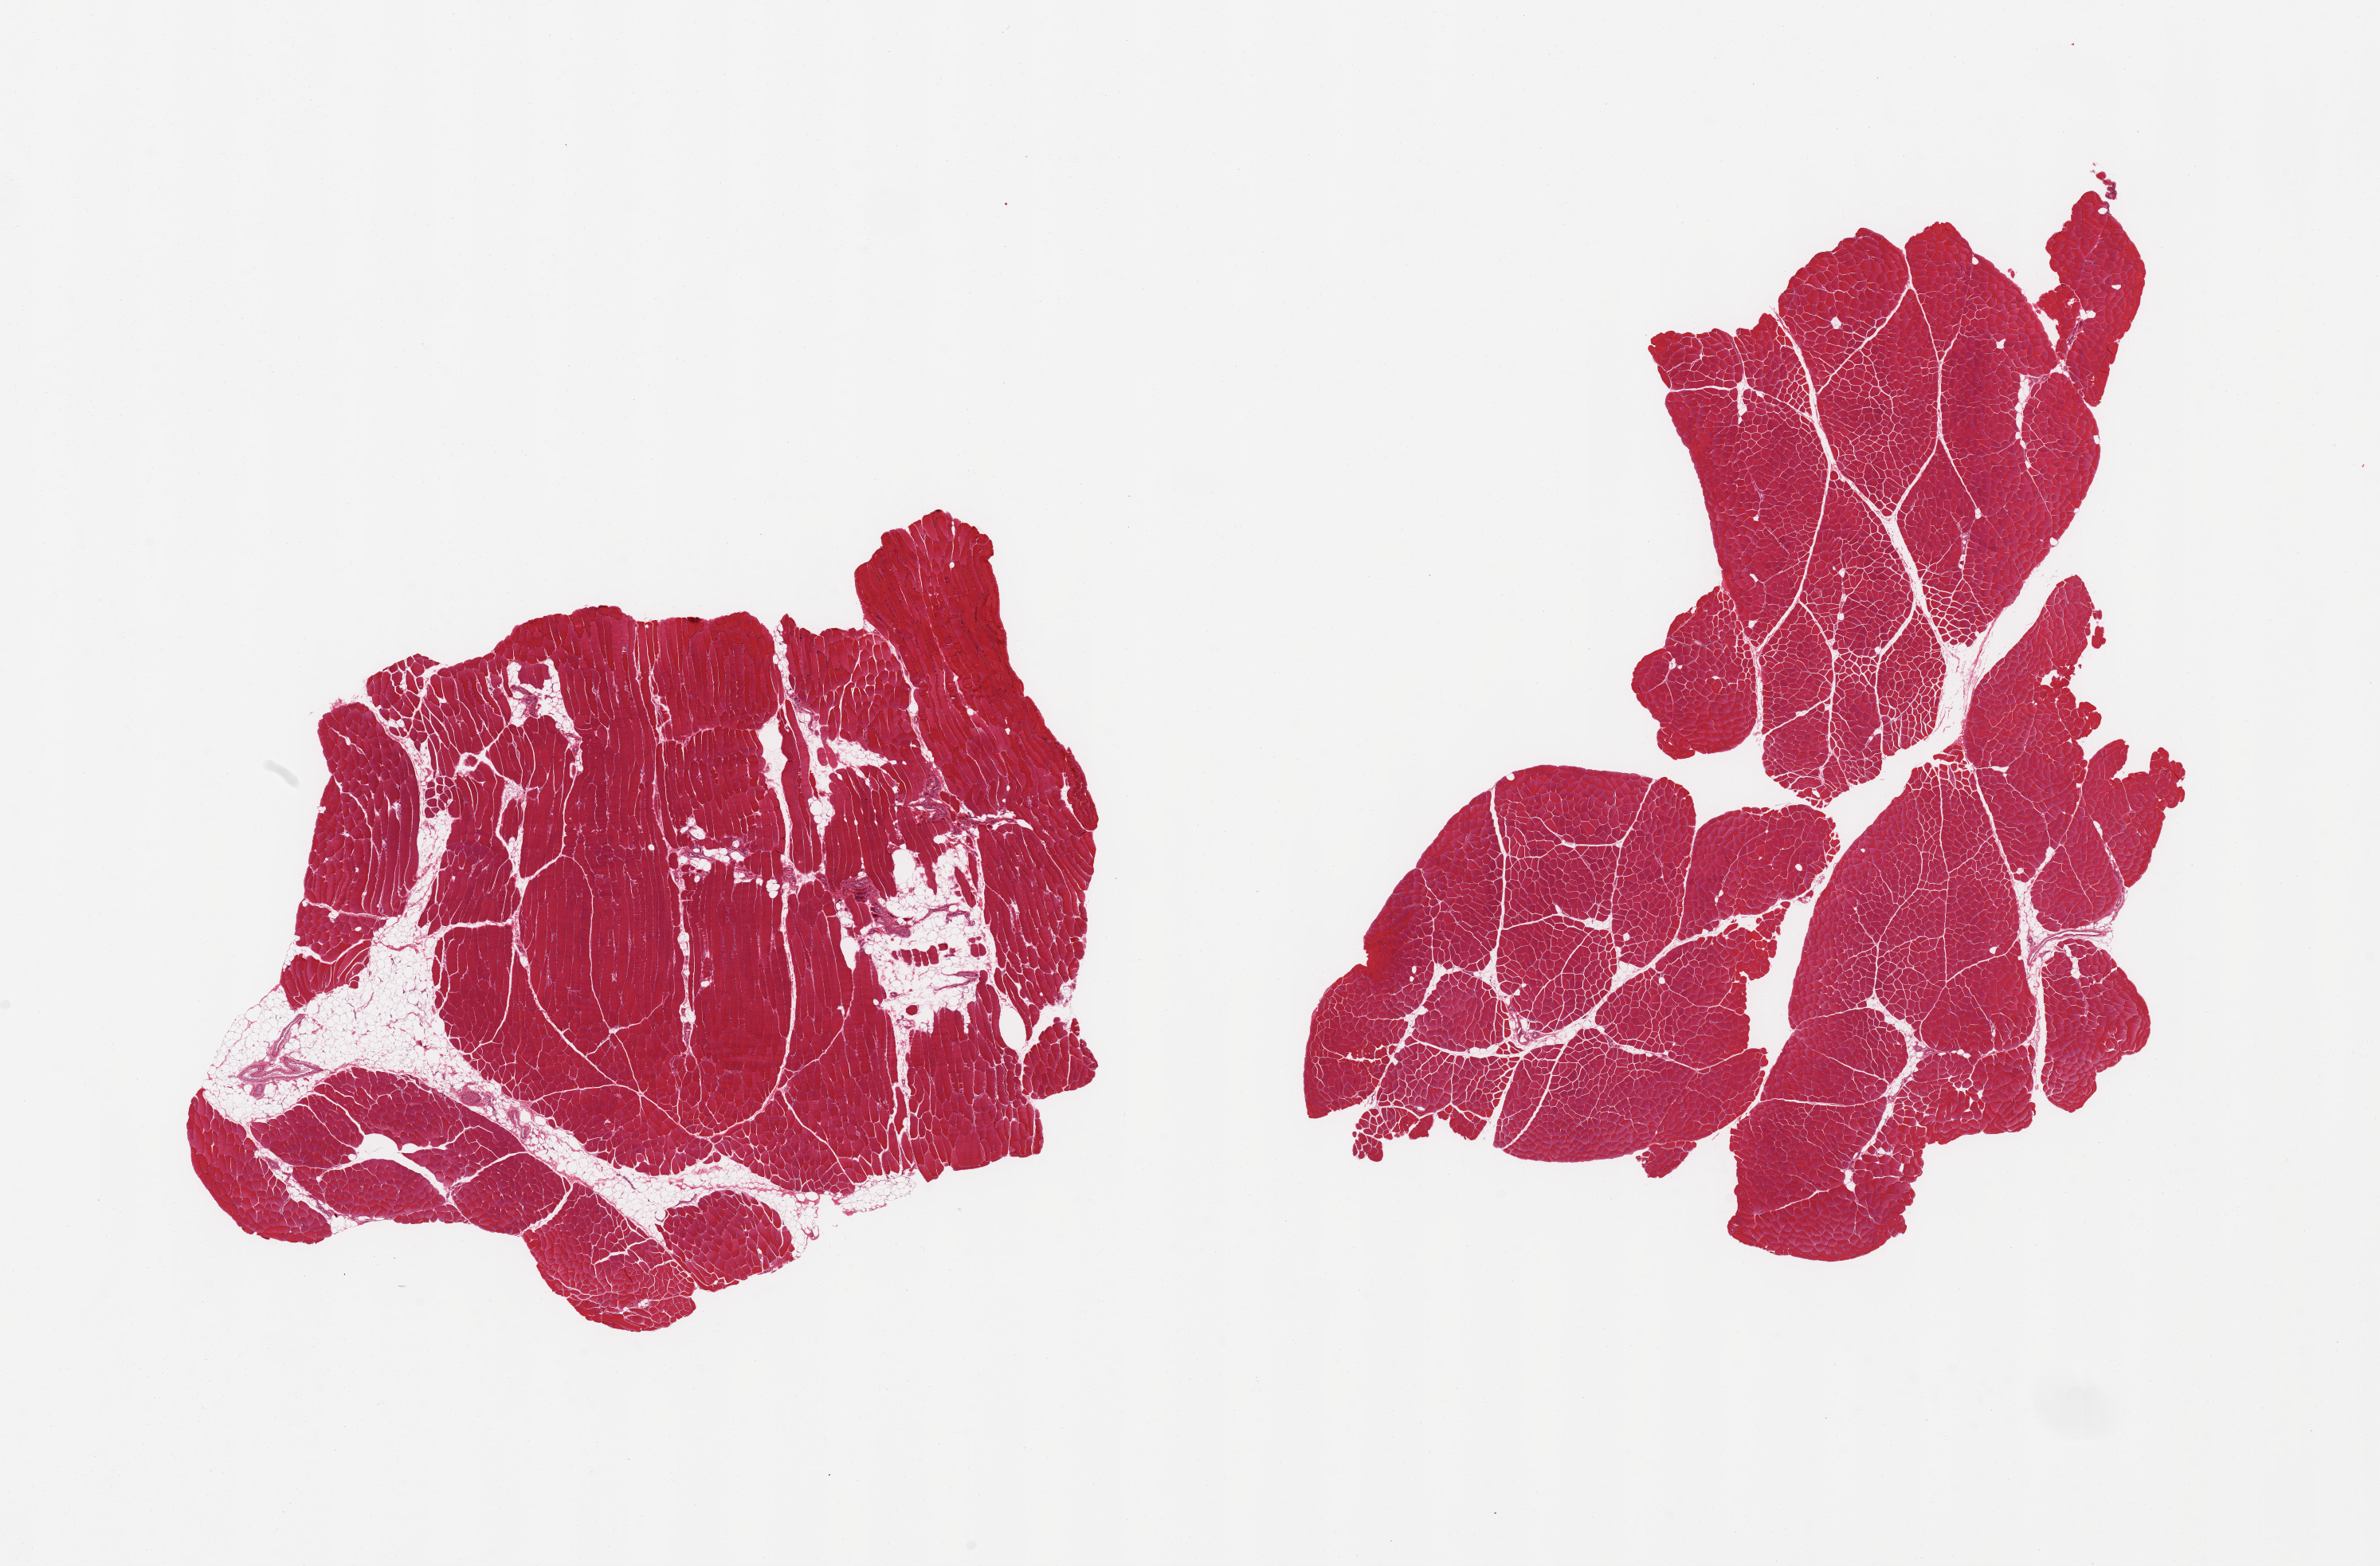
Haematoxylin and eosin whole-slide image, brightfield, shown as a low-resolution overview of the whole scanned area (about 23.6 x 15.5 mm); PAXgene-fixed paraffin-embedded (PFPE) section; sampled site (target tissue): skeletal muscle; donor tissue sample.
• pathologist's review note for this sample: 2 pieces, ~10% interstitial fat